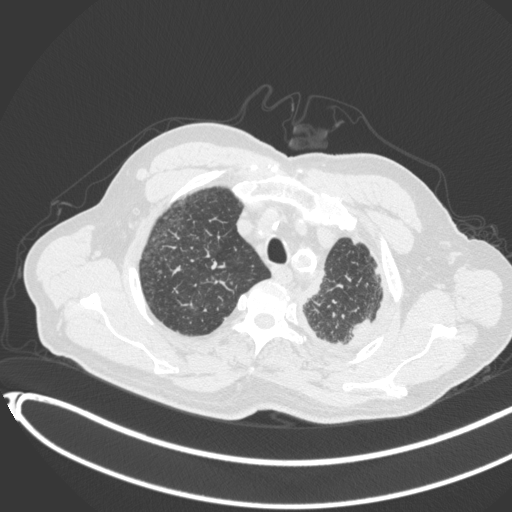
Chest CT, one axial slice. Position 363 of 451 along the scan axis. Lung window (W 1500 / L -600 HU). 512 × 512 image matrix, field of view 400 × 400 mm. Male patient, age 78 years. From the clinical record (not read from this slice): clinical TNM (as recorded): T1c N0 M1.
Structures marked on this image (rectangle marked by the reading radiologist):
- lung tumour (recorded histology: adenocarcinoma): bounding box <347,314,378,343> (left, top, right, bottom; pixels)